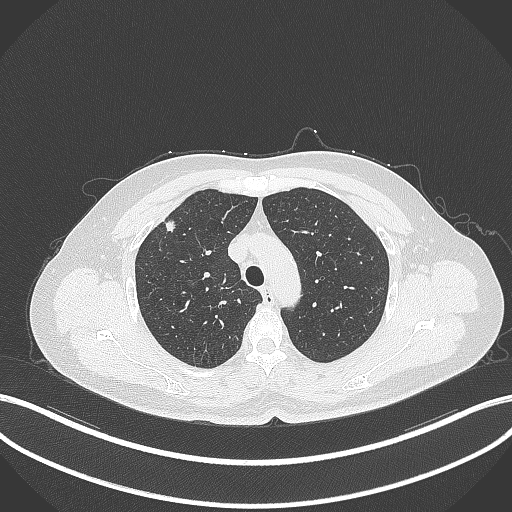
Chest CT, one axial slice. Slice 279 of 353 in the series (ordered by position). 120 kVp. Lung window (W 1500 / L -600 HU). 1 mm slice thickness. 512 × 512 image matrix. Patient: female, 56 years. From the clinical record (not read from this slice): clinical TNM (as recorded): T1c N0 M0.
Structures marked on this image (rectangle marked by the reading radiologist):
- lung tumour (recorded histology: adenocarcinoma): bounding box [x1, y1, x2, y2] px = [160, 215, 180, 235]